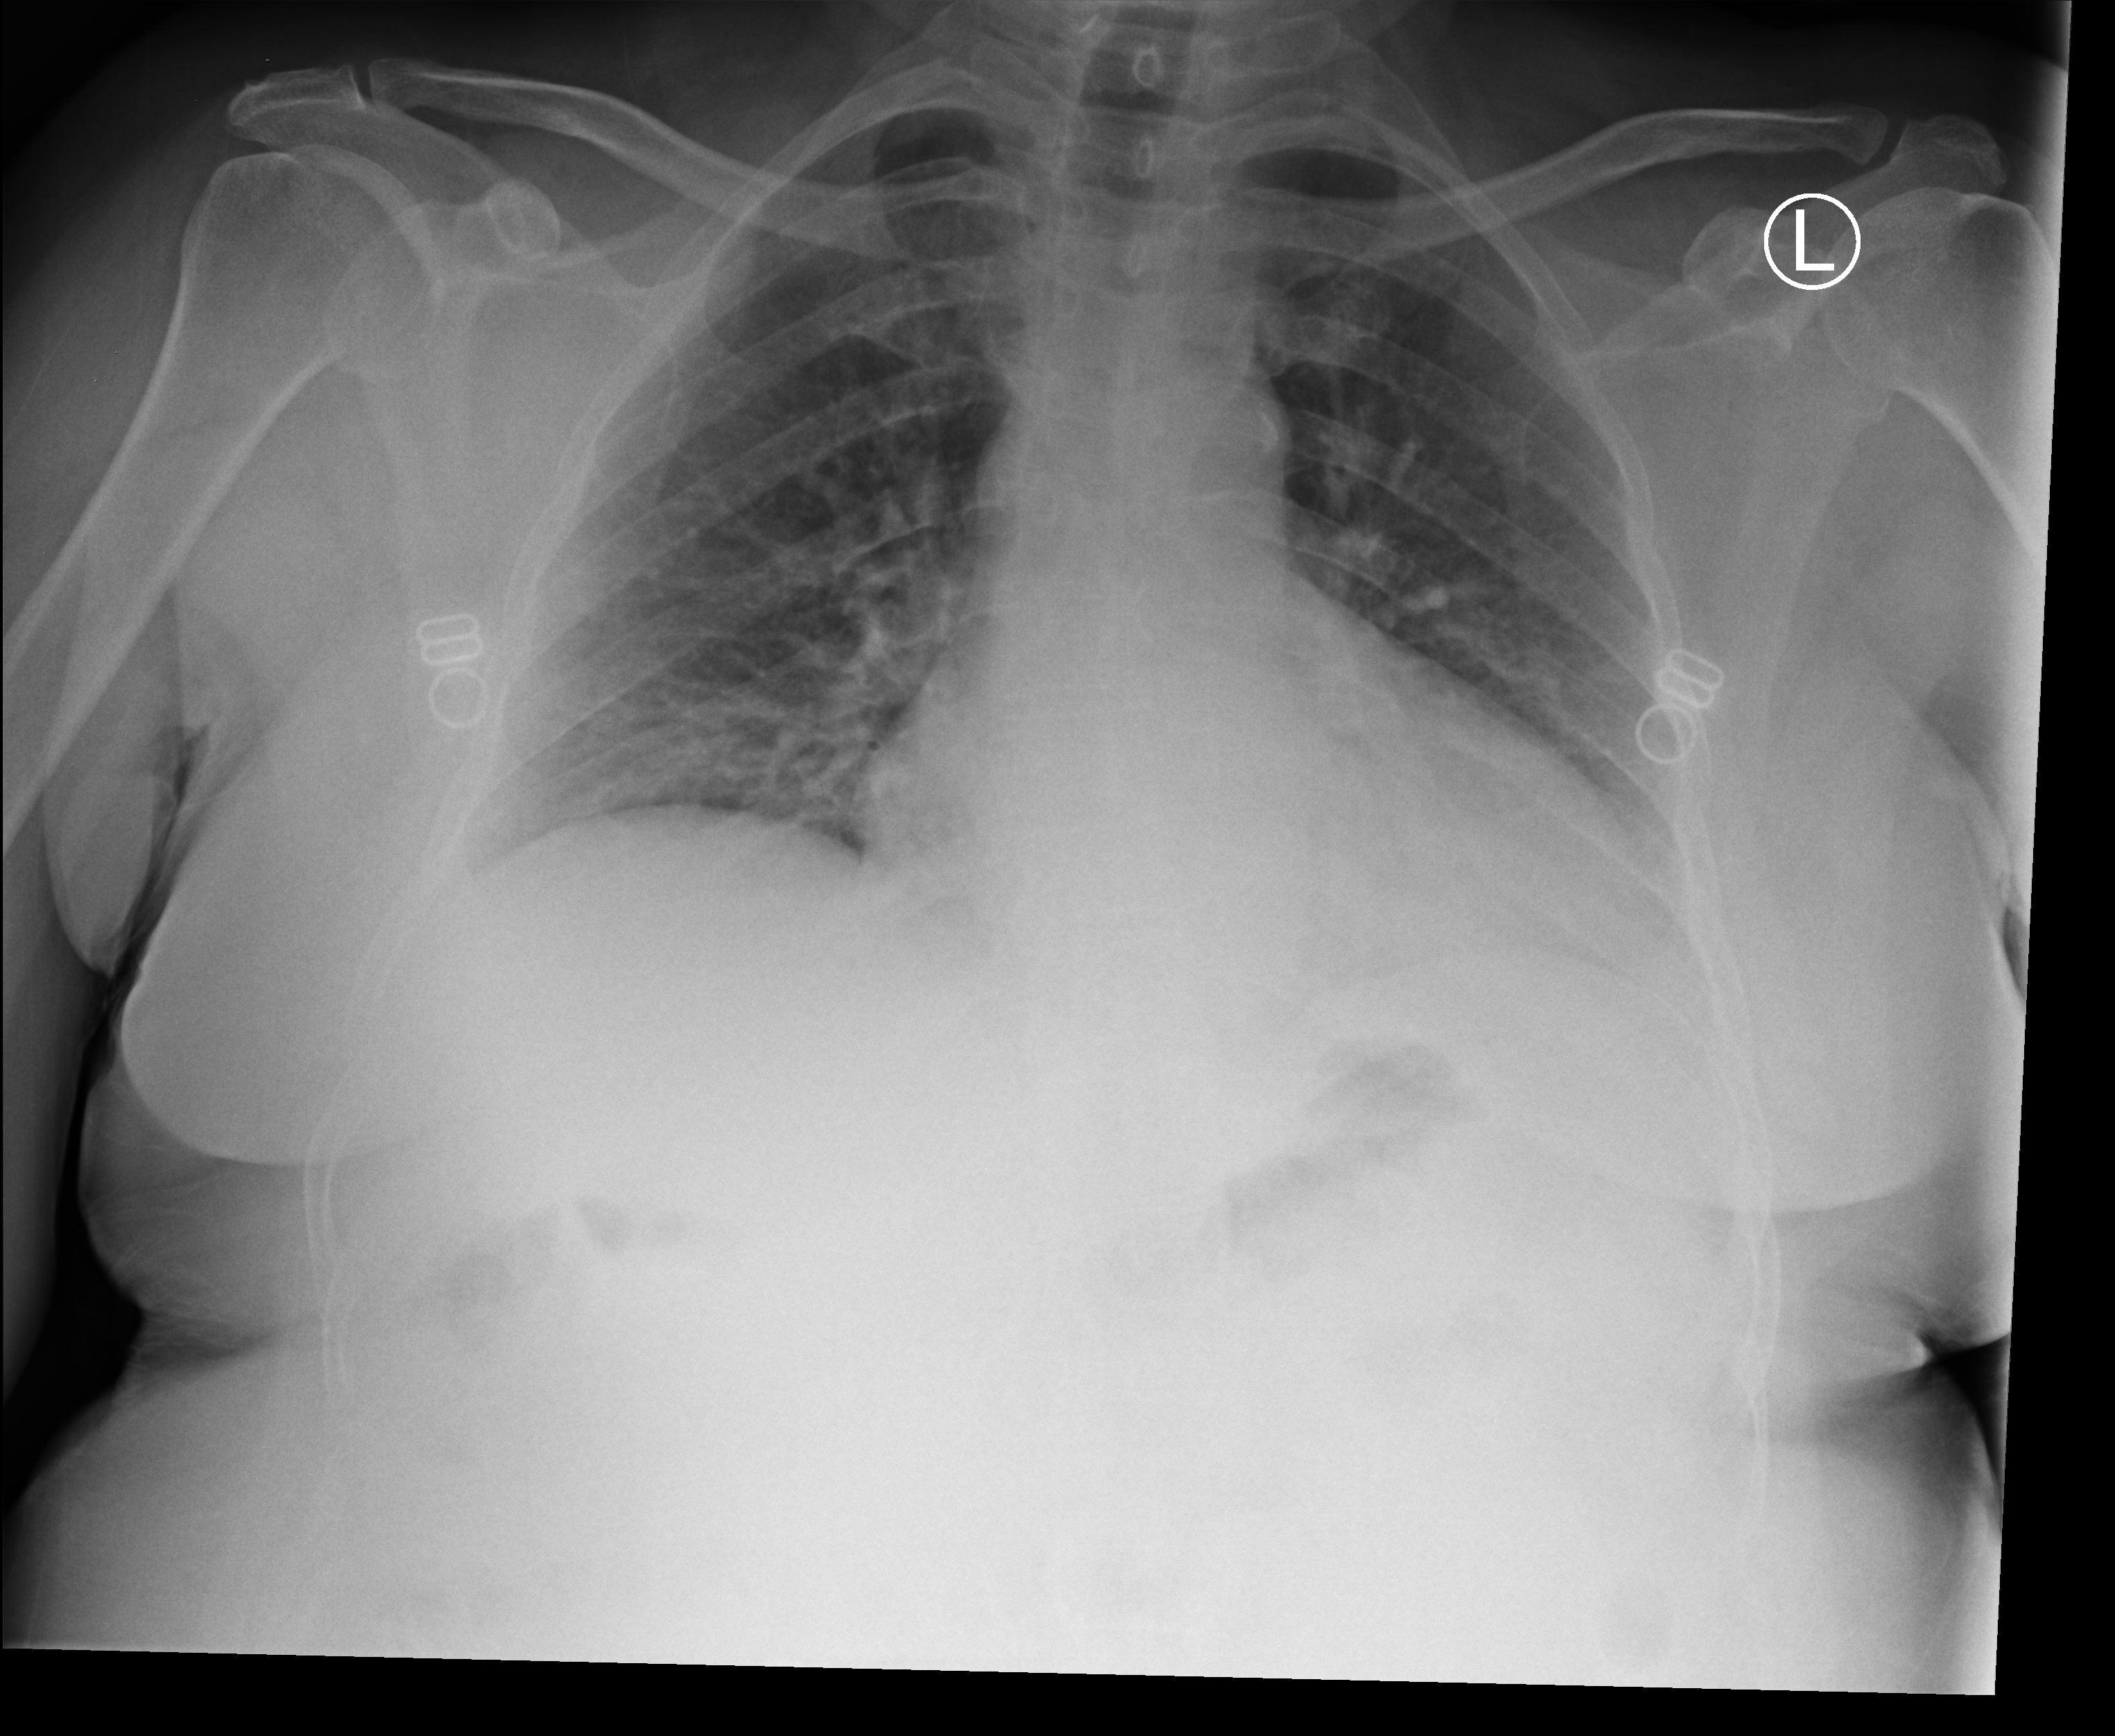
Chest X-ray (portable), anteroposterior (AP) projection. Patient hospitalised with COVID-19; female, aged 60–74 years.
Hospital-stay facts (about this admission, not read from this image; timing relative to this image not recorded): chronic kidney disease (admission record): no; diabetes (admission record): no.